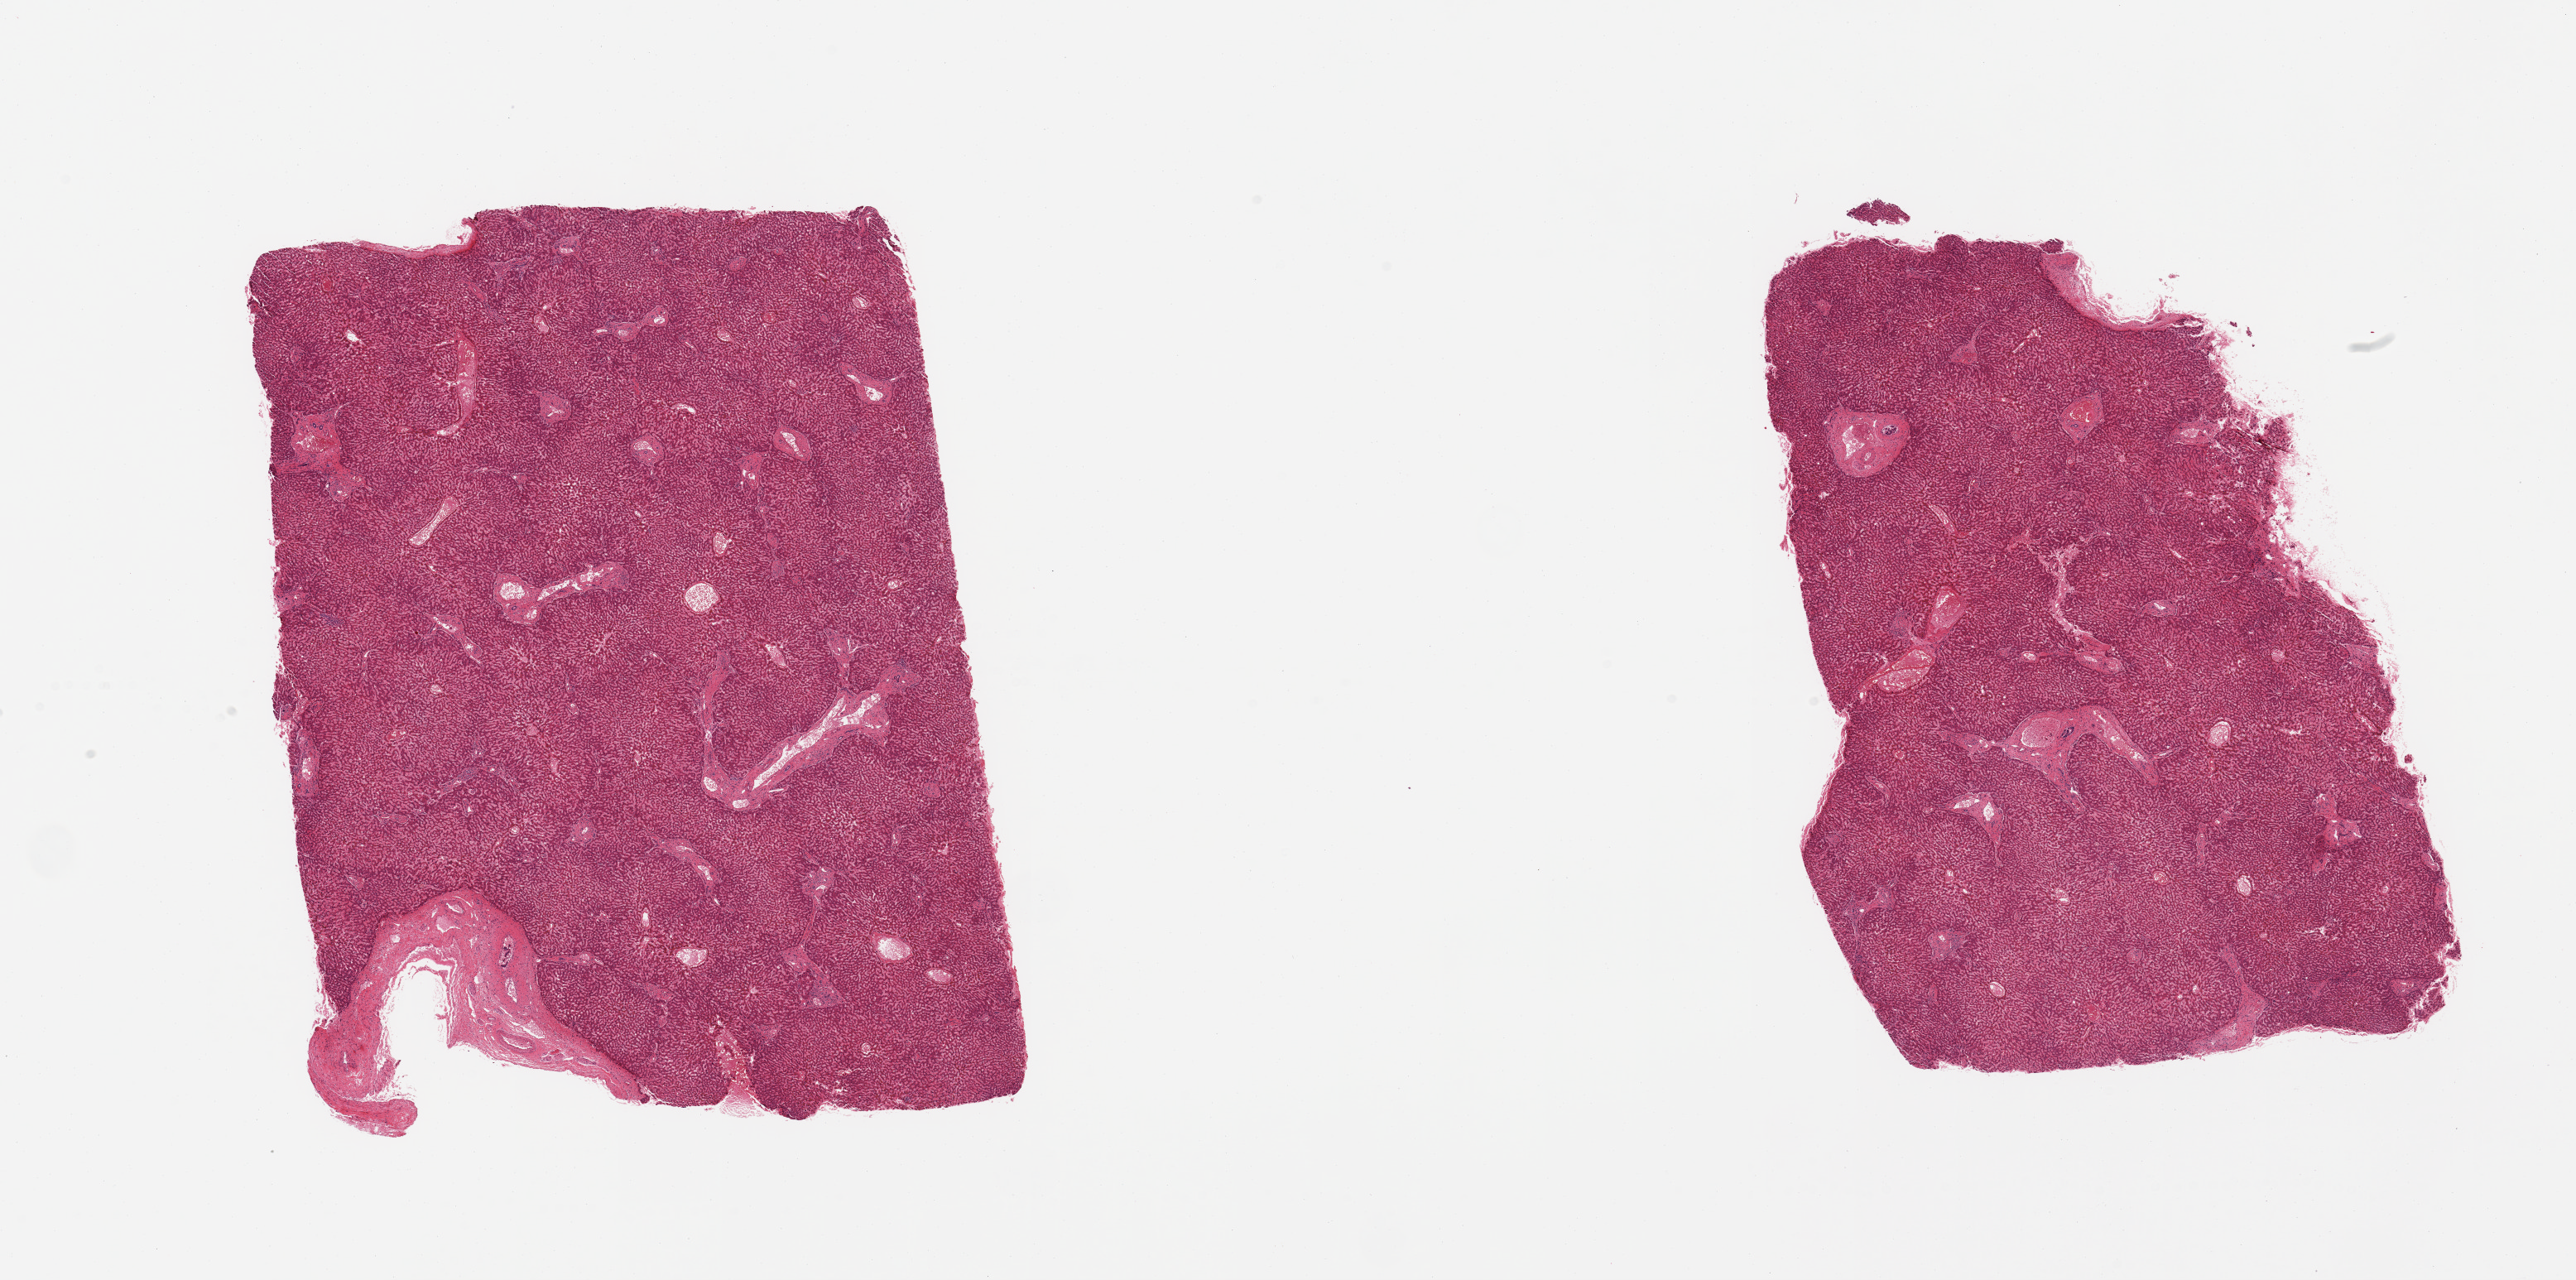
Hematoxylin and eosin (H&E) whole-slide image — whole scanned area (about 24.6 x 12.2 mm) shown as a low-resolution overview; PAXgene-fixed paraffin-embedded (PFPE) section; target tissue: liver; donor tissue sample. Male donor.
Review note (as recorded): 2 pieces; congestion; distended sinusoids and fine droplets of bile in cytoplasm of the liver cells.